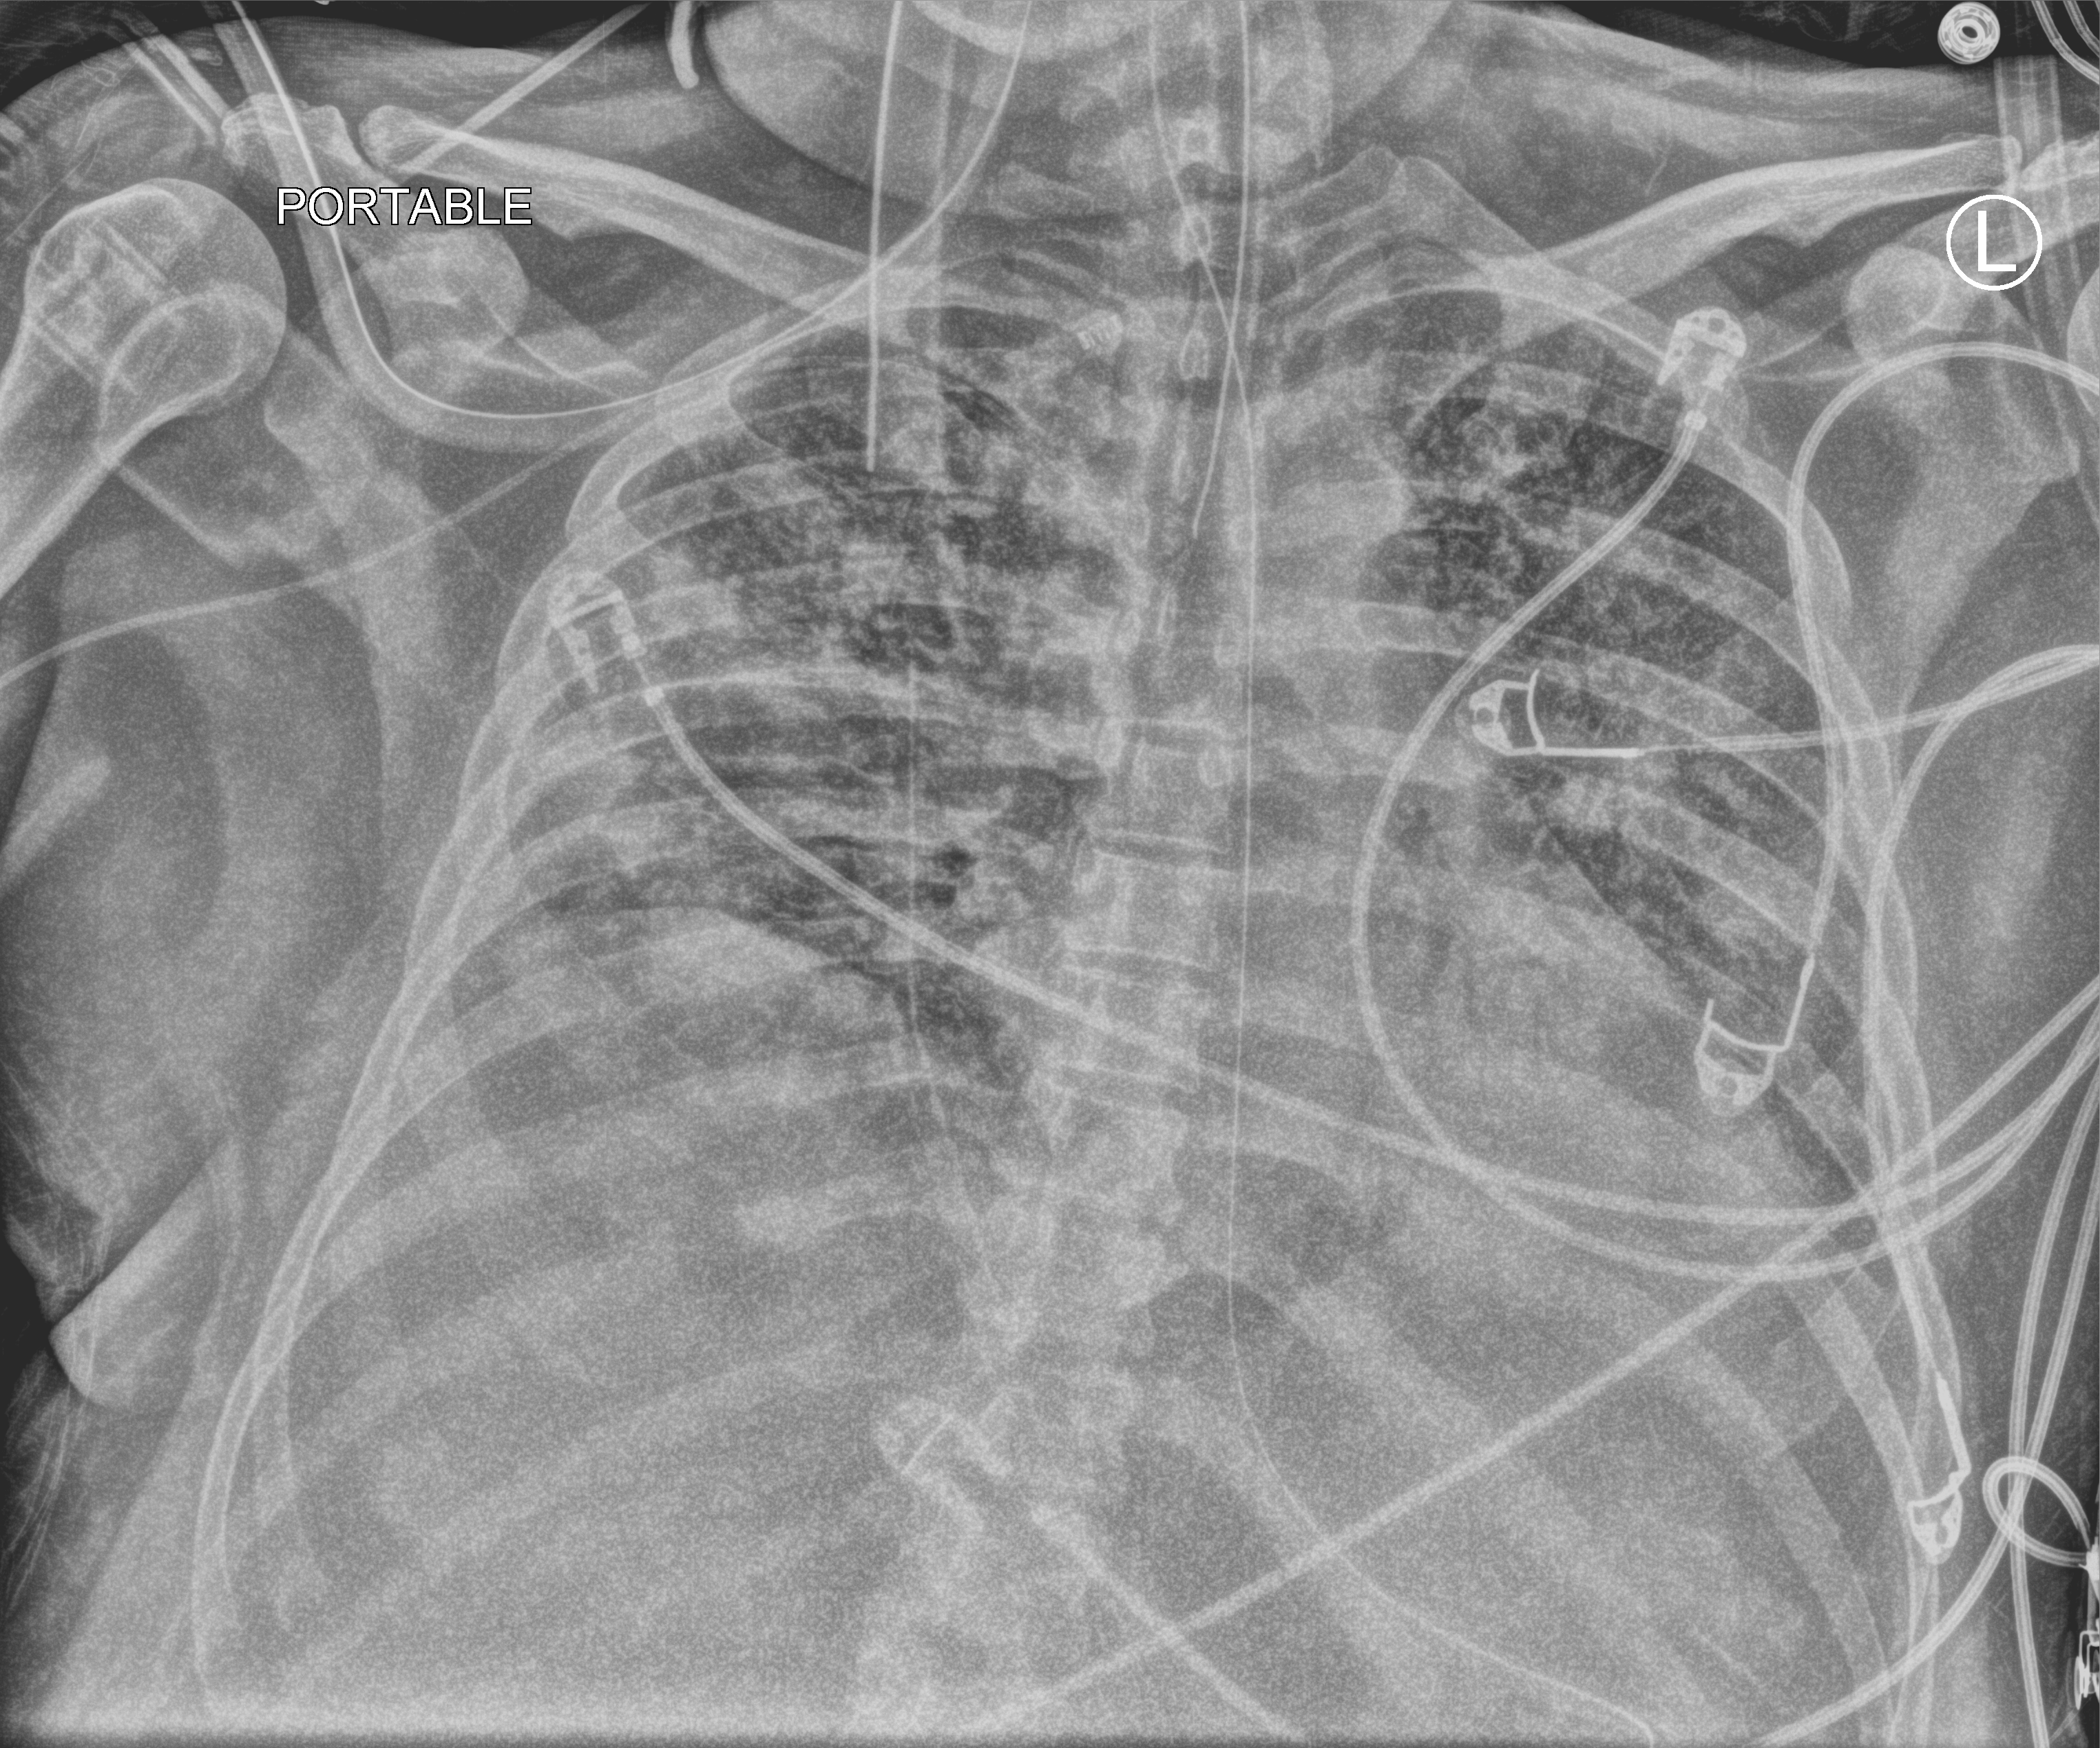
Portable chest radiograph, anteroposterior (AP) projection. Male patient hospitalised with COVID-19, age 18–59 years.
Hospital-stay facts (about this admission, not read from this image; timing relative to this image not recorded):
- other chronic lung disease (admission record): no
- mechanically ventilated during this hospital stay: yes